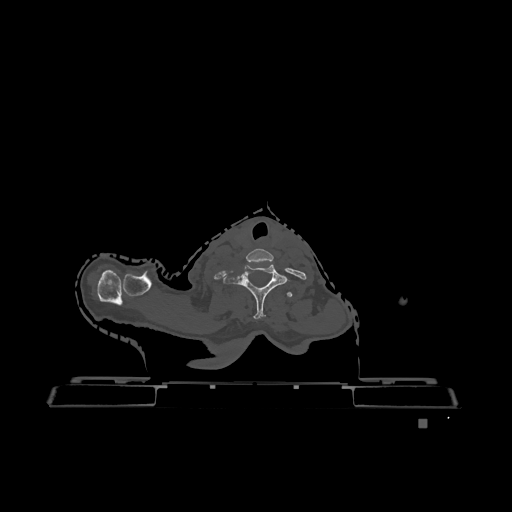
CT including the spine, one axial slice. Slice 1029 of 1317 in the series (ordered by position). Bone window (W 1800 / L 400 HU). 0.5 mm slice thickness. 512 × 512 image matrix, field of view 500 × 500 mm. Patient: female, 74 years. Case-level facts recorded for this patient, not image findings: primary cancer: lung.
Annotated regions visible in this slice (semi-automatic segmentation, software-assisted and operator-edited):
- T1 vertebra: box from (x=287, y=292) to (x=293, y=297) px